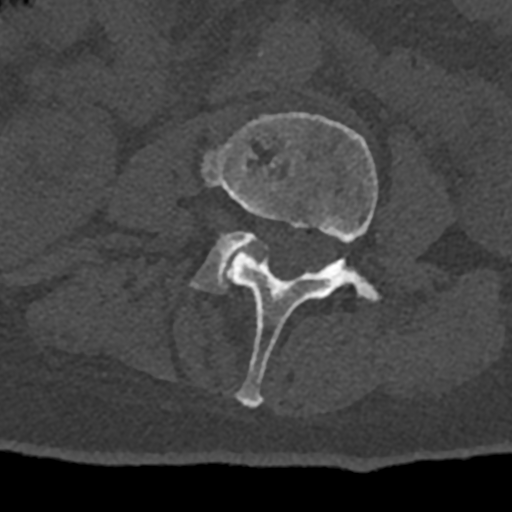
CT including the spine, one axial slice; 120 kVp; bone window (W 1800 / L 400 HU); 512 × 512 image matrix. Patient: male, 74 years. From the clinical record (not read from this slice): primary cancer: renal.
Structures marked on this image (semi-automatic segmentation, software-assisted and operator-edited):
- L3 vertebra: bounding box (x1, y1, x2, y2) in pixels: (202, 113, 380, 408)
- L4 vertebra: (192, 231, 267, 293)